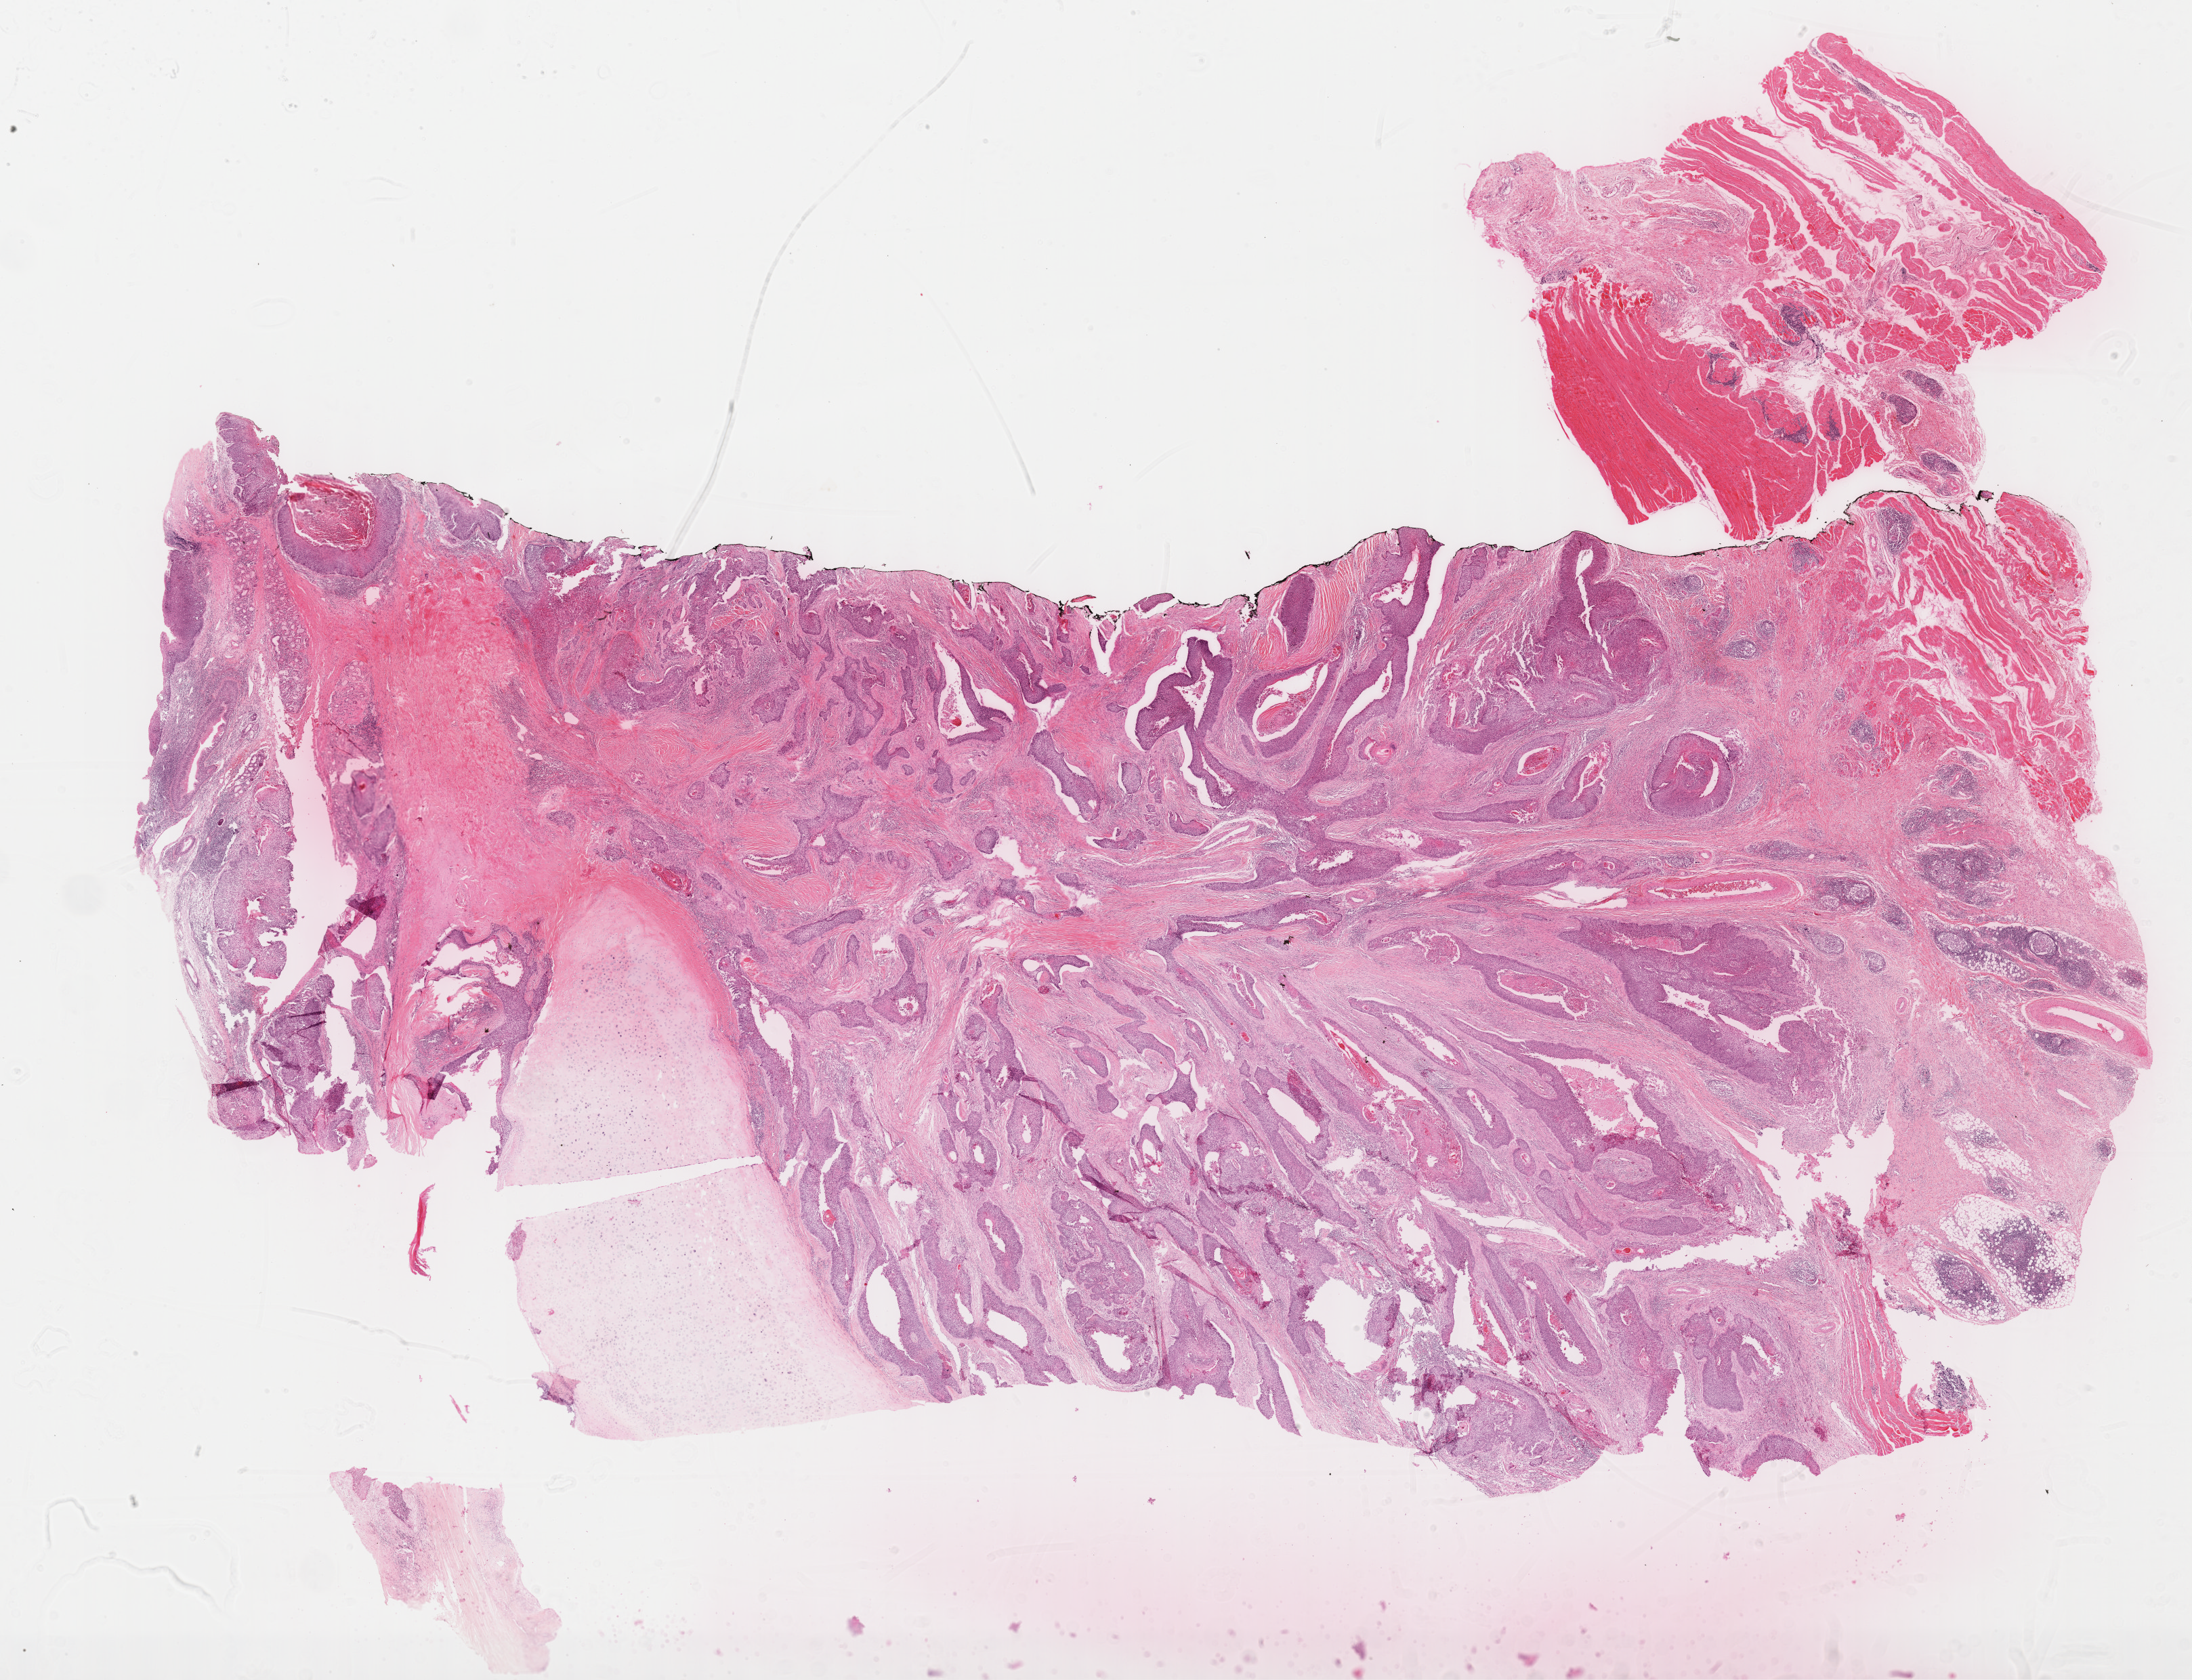
Digitized Hematoxylin and eosin (H&E) stained tissue section (whole slide), shown as a low-resolution overview of the whole scanned area (about 26.2 x 20.1 mm), formalin-fixed paraffin-embedded (FFPE) diagnostic section, primary tumour sample from the head and neck. Female, age 60 years at initial diagnosis. Histologic grade: G3 (poorly differentiated).
TNM: T4a N1. Histologic diagnosis: Squamous cell carcinoma, NOS (larynx, NOS). Laterality: right. Lymph nodes positive (case pathology): 1 of 27 examined. AJCC pathologic stage: IVA (7th edition).